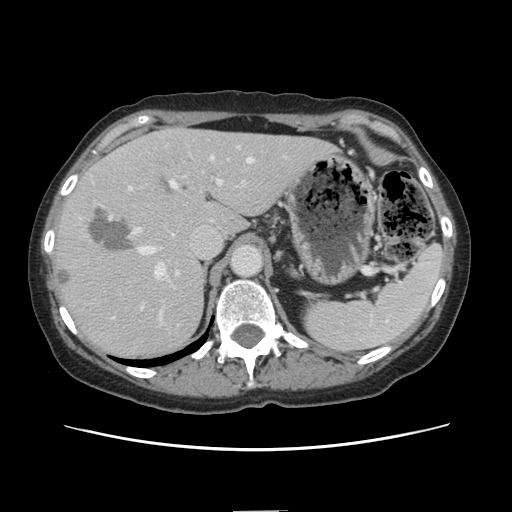
Contrast-enhanced abdominal CT, one axial slice; position 99 of 141 along the scan axis; 120 kVp; intravenous contrast given; soft-tissue window (W 400 / L 40 HU); 512 × 512 image matrix, field of view 350 × 350 mm. Female patient, age 63 years. Case-level facts recorded for this patient, not image findings: diagnosis: colorectal cancer liver metastases, imaged before liver resection.
Structures marked on this image (outlined manually by an expert reader):
- hepatic veins: box from (x=139, y=157) to (x=253, y=277) px
- liver: (x=52, y=129)–(x=332, y=360)
- planned liver remnant (the part of the liver to remain after resection): (x=185, y=130)–(x=333, y=238)
- portal vein (with intrahepatic branches): (x=127, y=180)–(x=222, y=274)